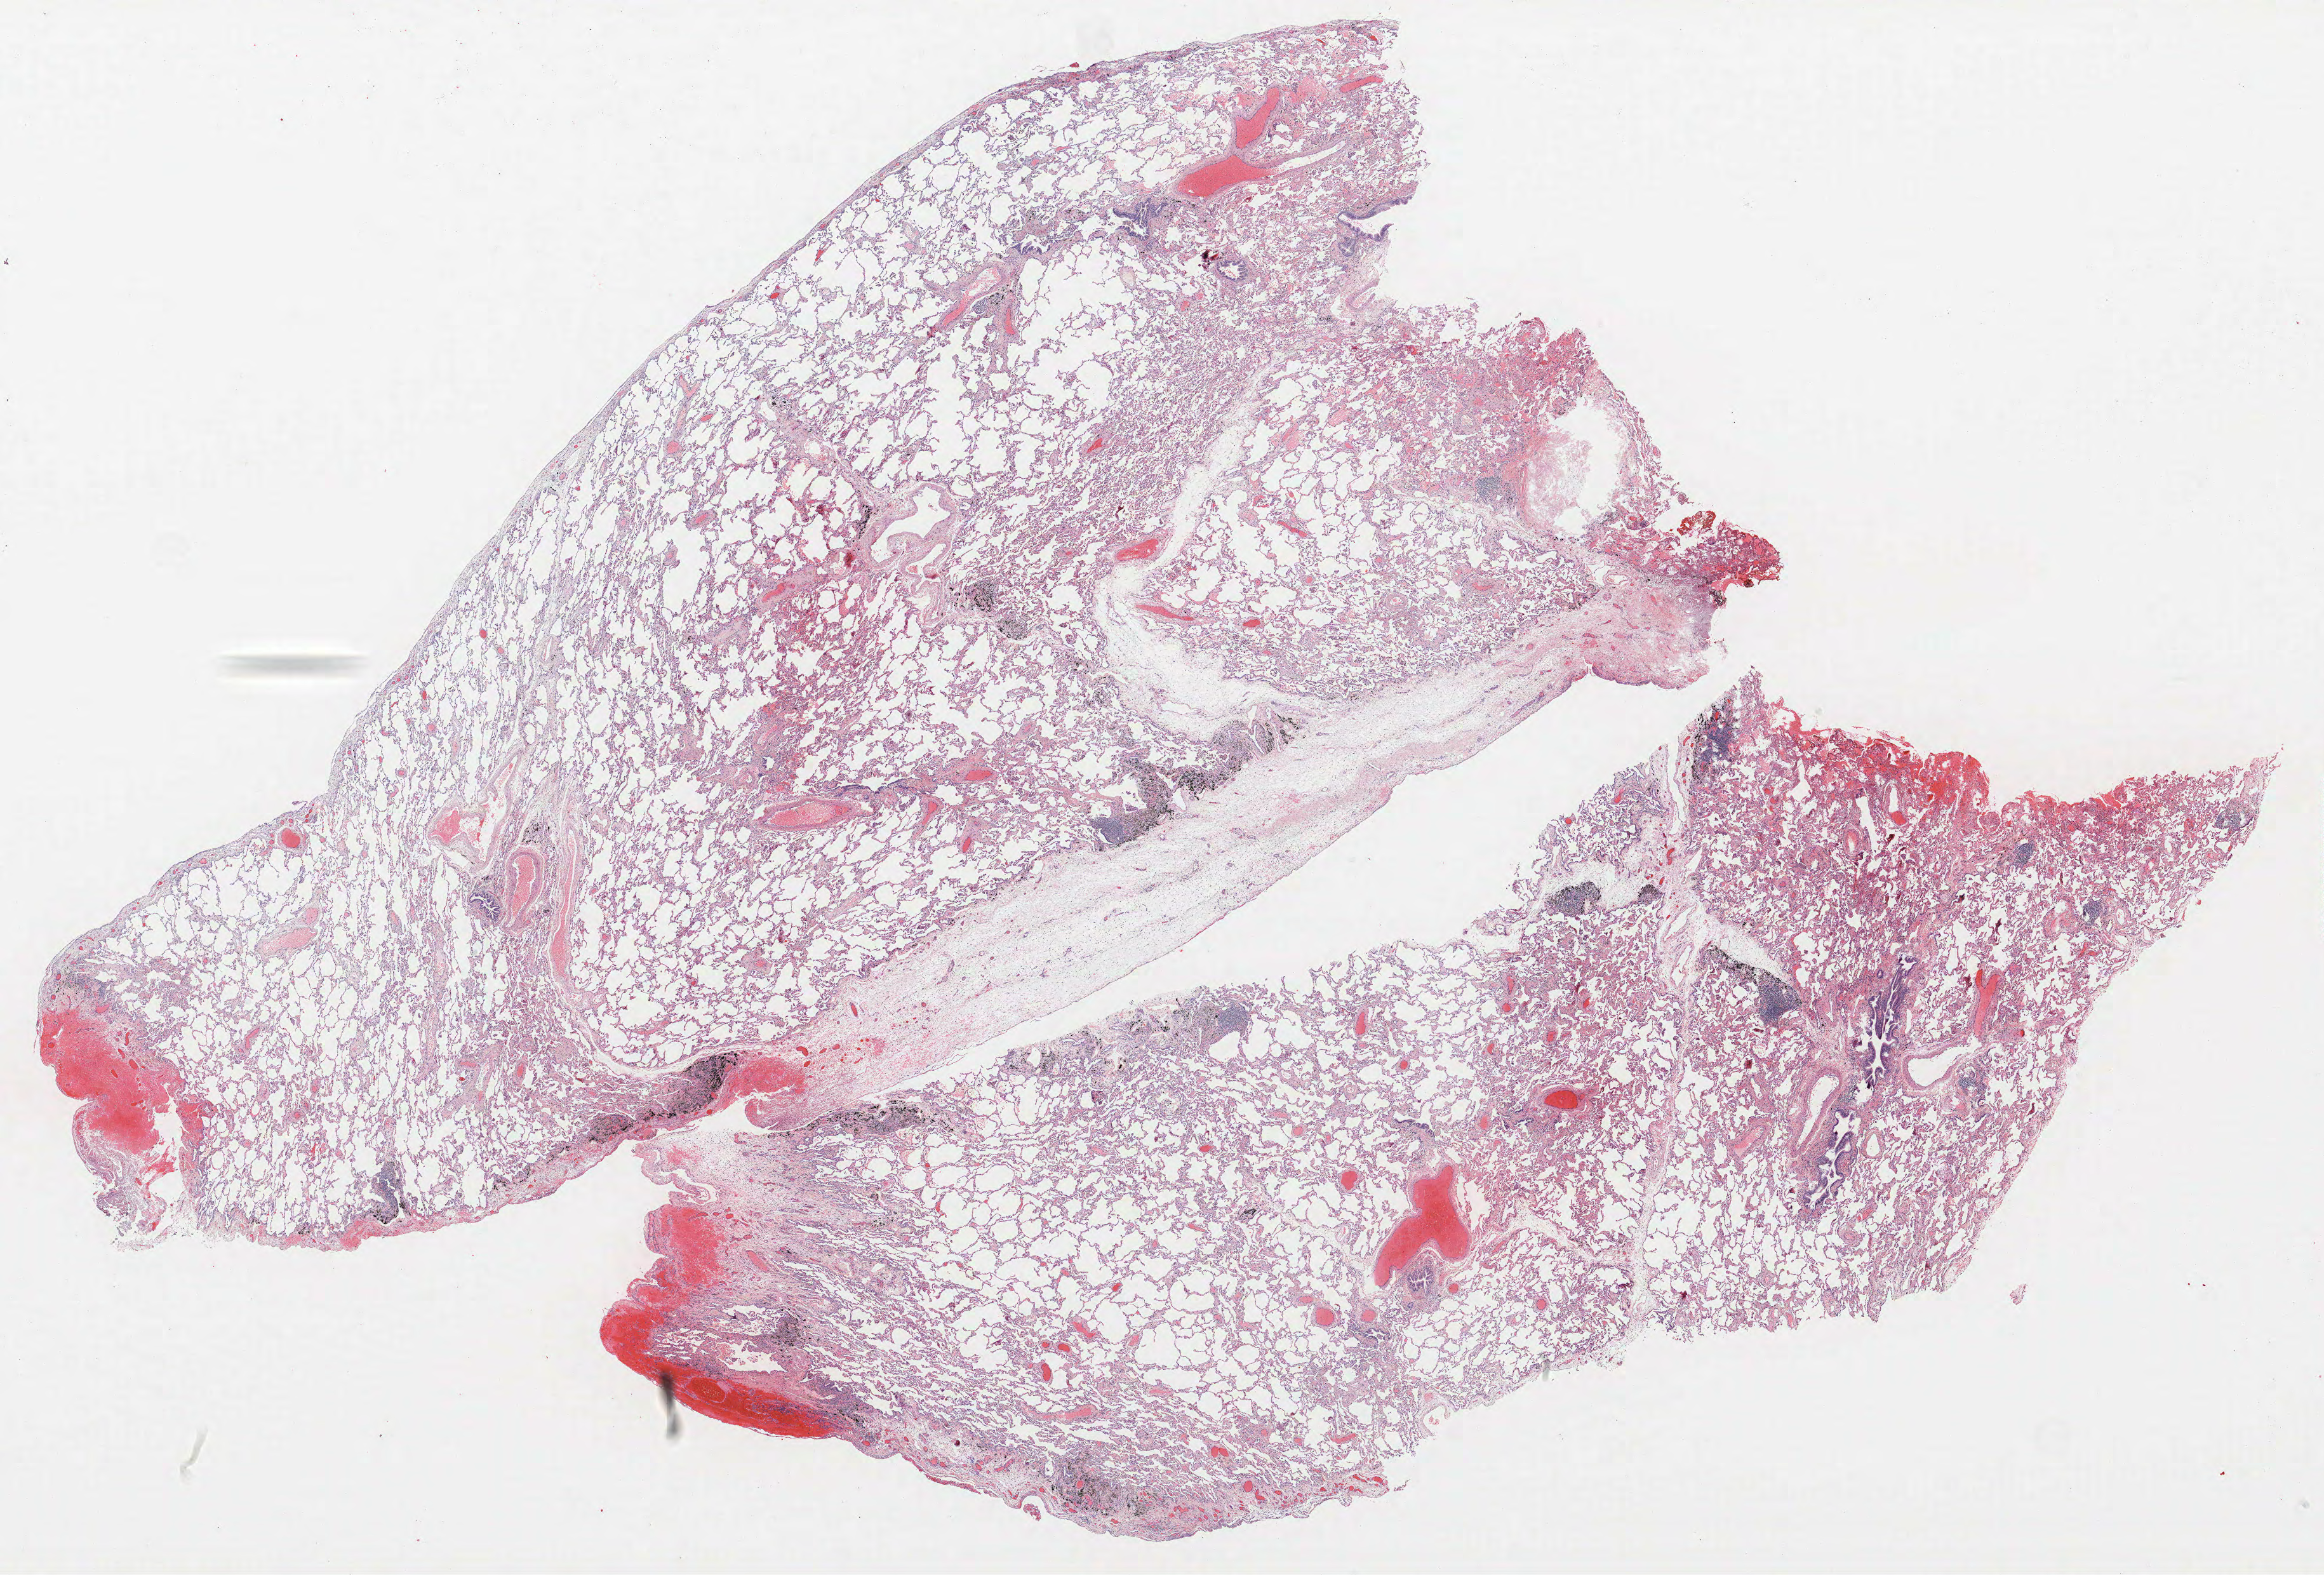
H&E whole-slide image — shown as a low-resolution overview of the whole scanned area (about 29.3 x 19.8 mm, acquisition: 40x scan), FFPE section, lung. Female patient, aged 61 at enrolment. Current smoker at enrolment.
Participant's lung-cancer diagnosis: Adenocarcinoma, NOS.